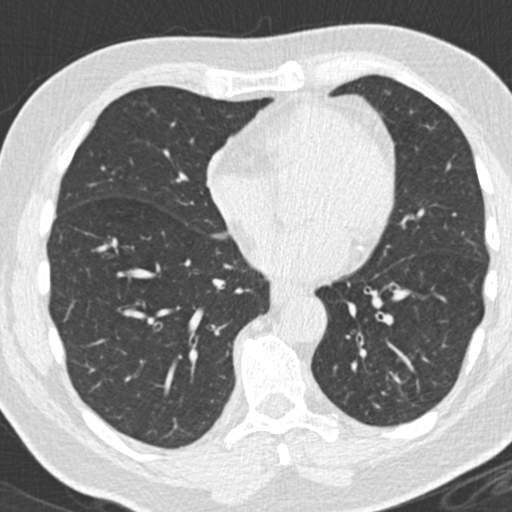
Chest CT (low-dose screening protocol), one axial image, third screening round (two years after baseline), lung window (W 1500 / L -600 HU), 512 × 512 image matrix, field of view 300 × 300 mm. Male, age 66 years at enrolment. Former smoker at enrolment.
Lesion marked by an expert reader, bounding box <354,342,428,430> (left, top, right, bottom; pixels). Reader record for this screening exam (exam-level; its link to the box is not recorded): non-calcified nodule or mass ≥4 mm, left lower lobe, 31 × 24 mm, spiculated (stellate) margins, pre-existing on the prior screen: yes; interval growth: yes. Official screen result: positive, other.